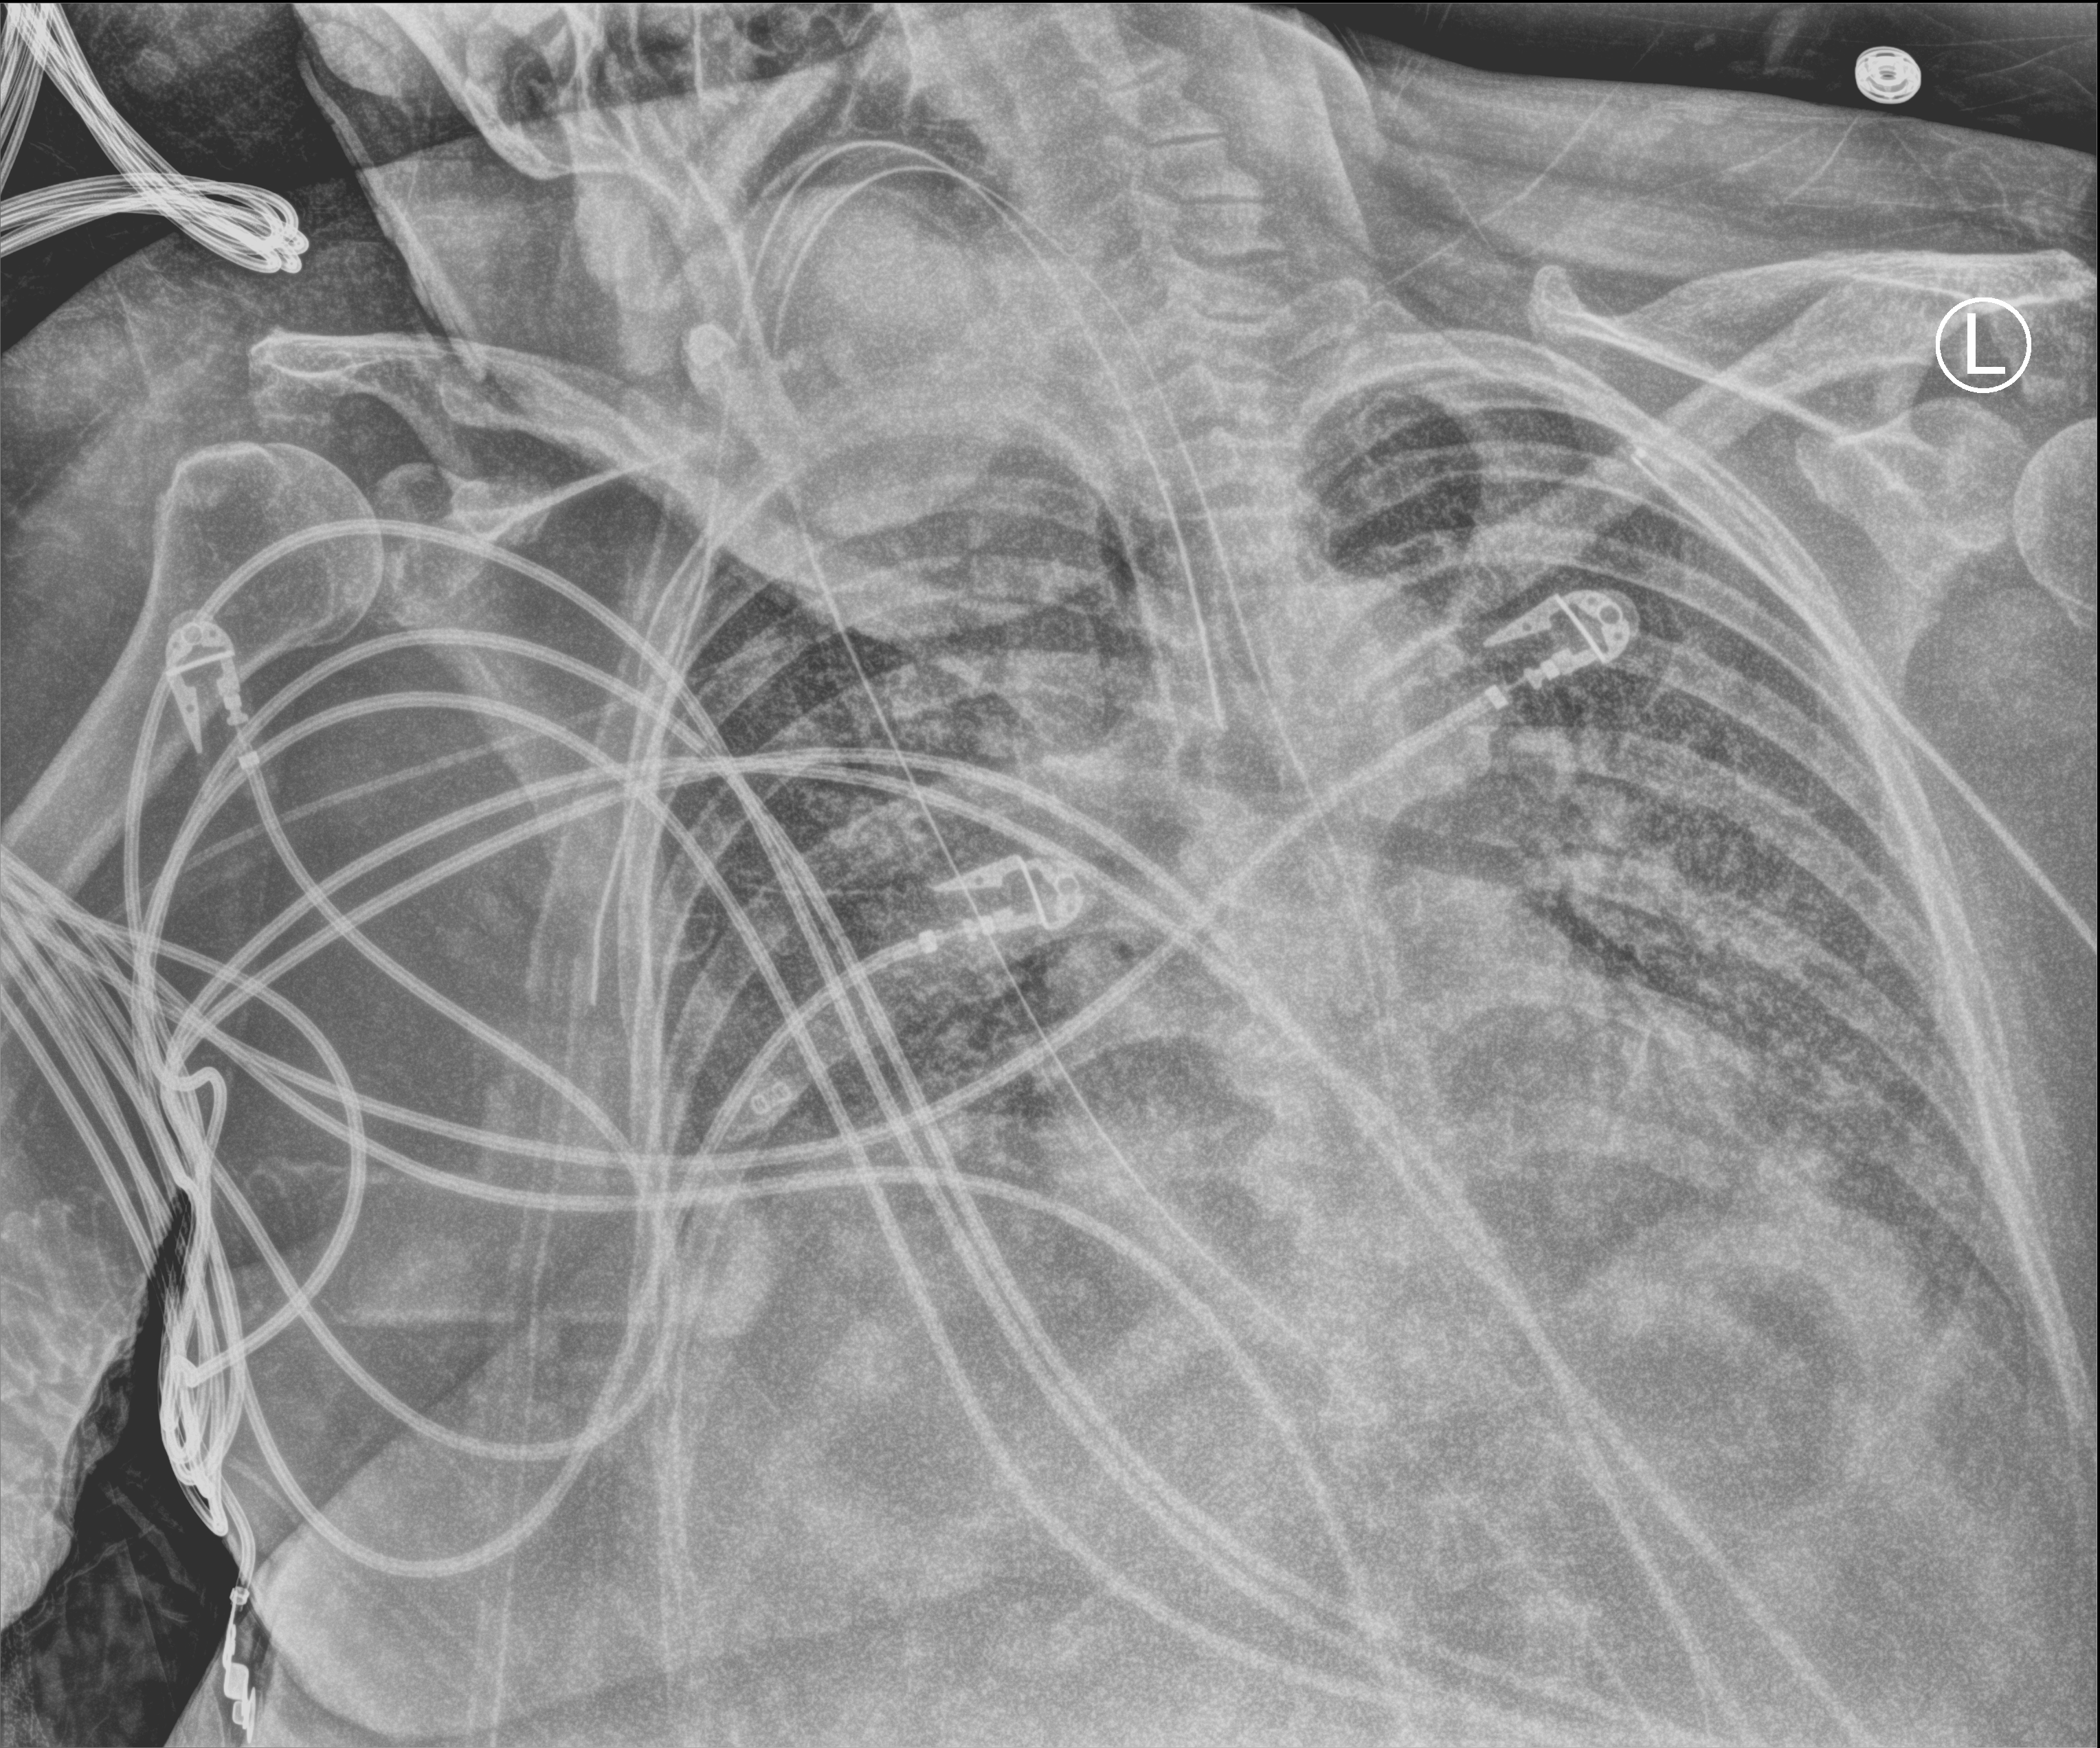
Chest X-ray (portable), anteroposterior (AP) projection. Female patient hospitalised with COVID-19, age 60–74 years.
Hospital-stay facts (about this admission, not read from this image; timing relative to this image not recorded): mechanically ventilated during this hospital stay: yes.